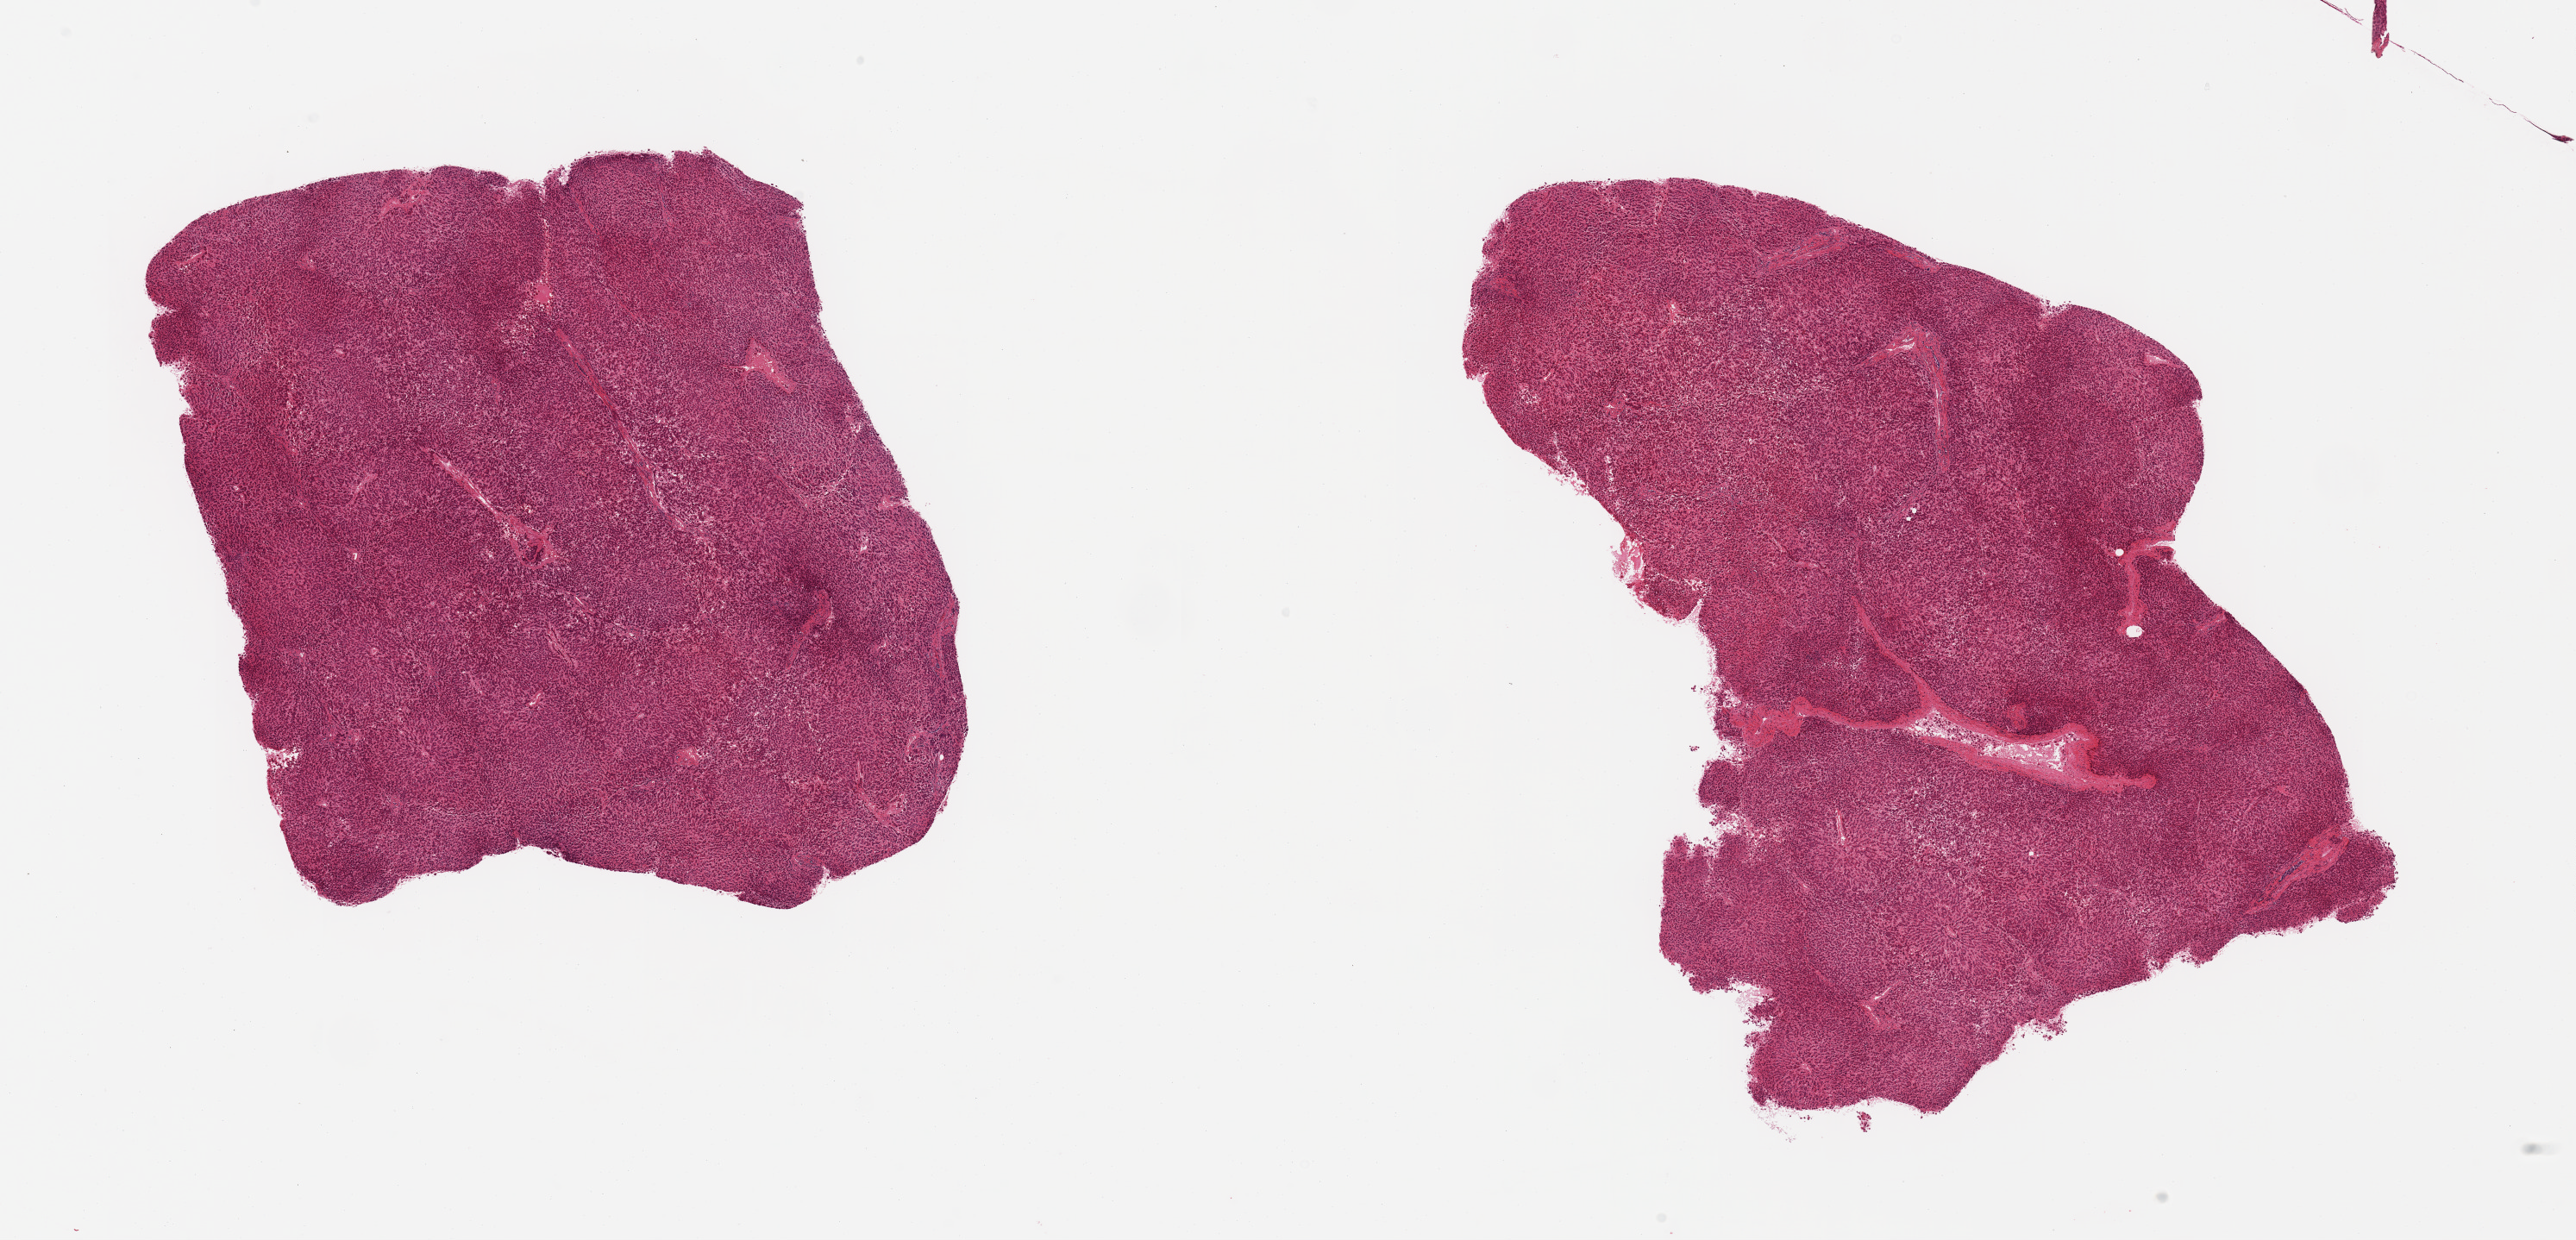
Whole-slide image, H&E stain, whole scanned area (about 23.6 x 11.4 mm, slide scanned at 20x) shown as a low-resolution overview. PAXgene-fixed, paraffin-embedded tissue. Sampled site (target tissue): liver. Tissue donor sample. Donor: female.
Pathologist's review note for this sample: 2 pieces; congestion.